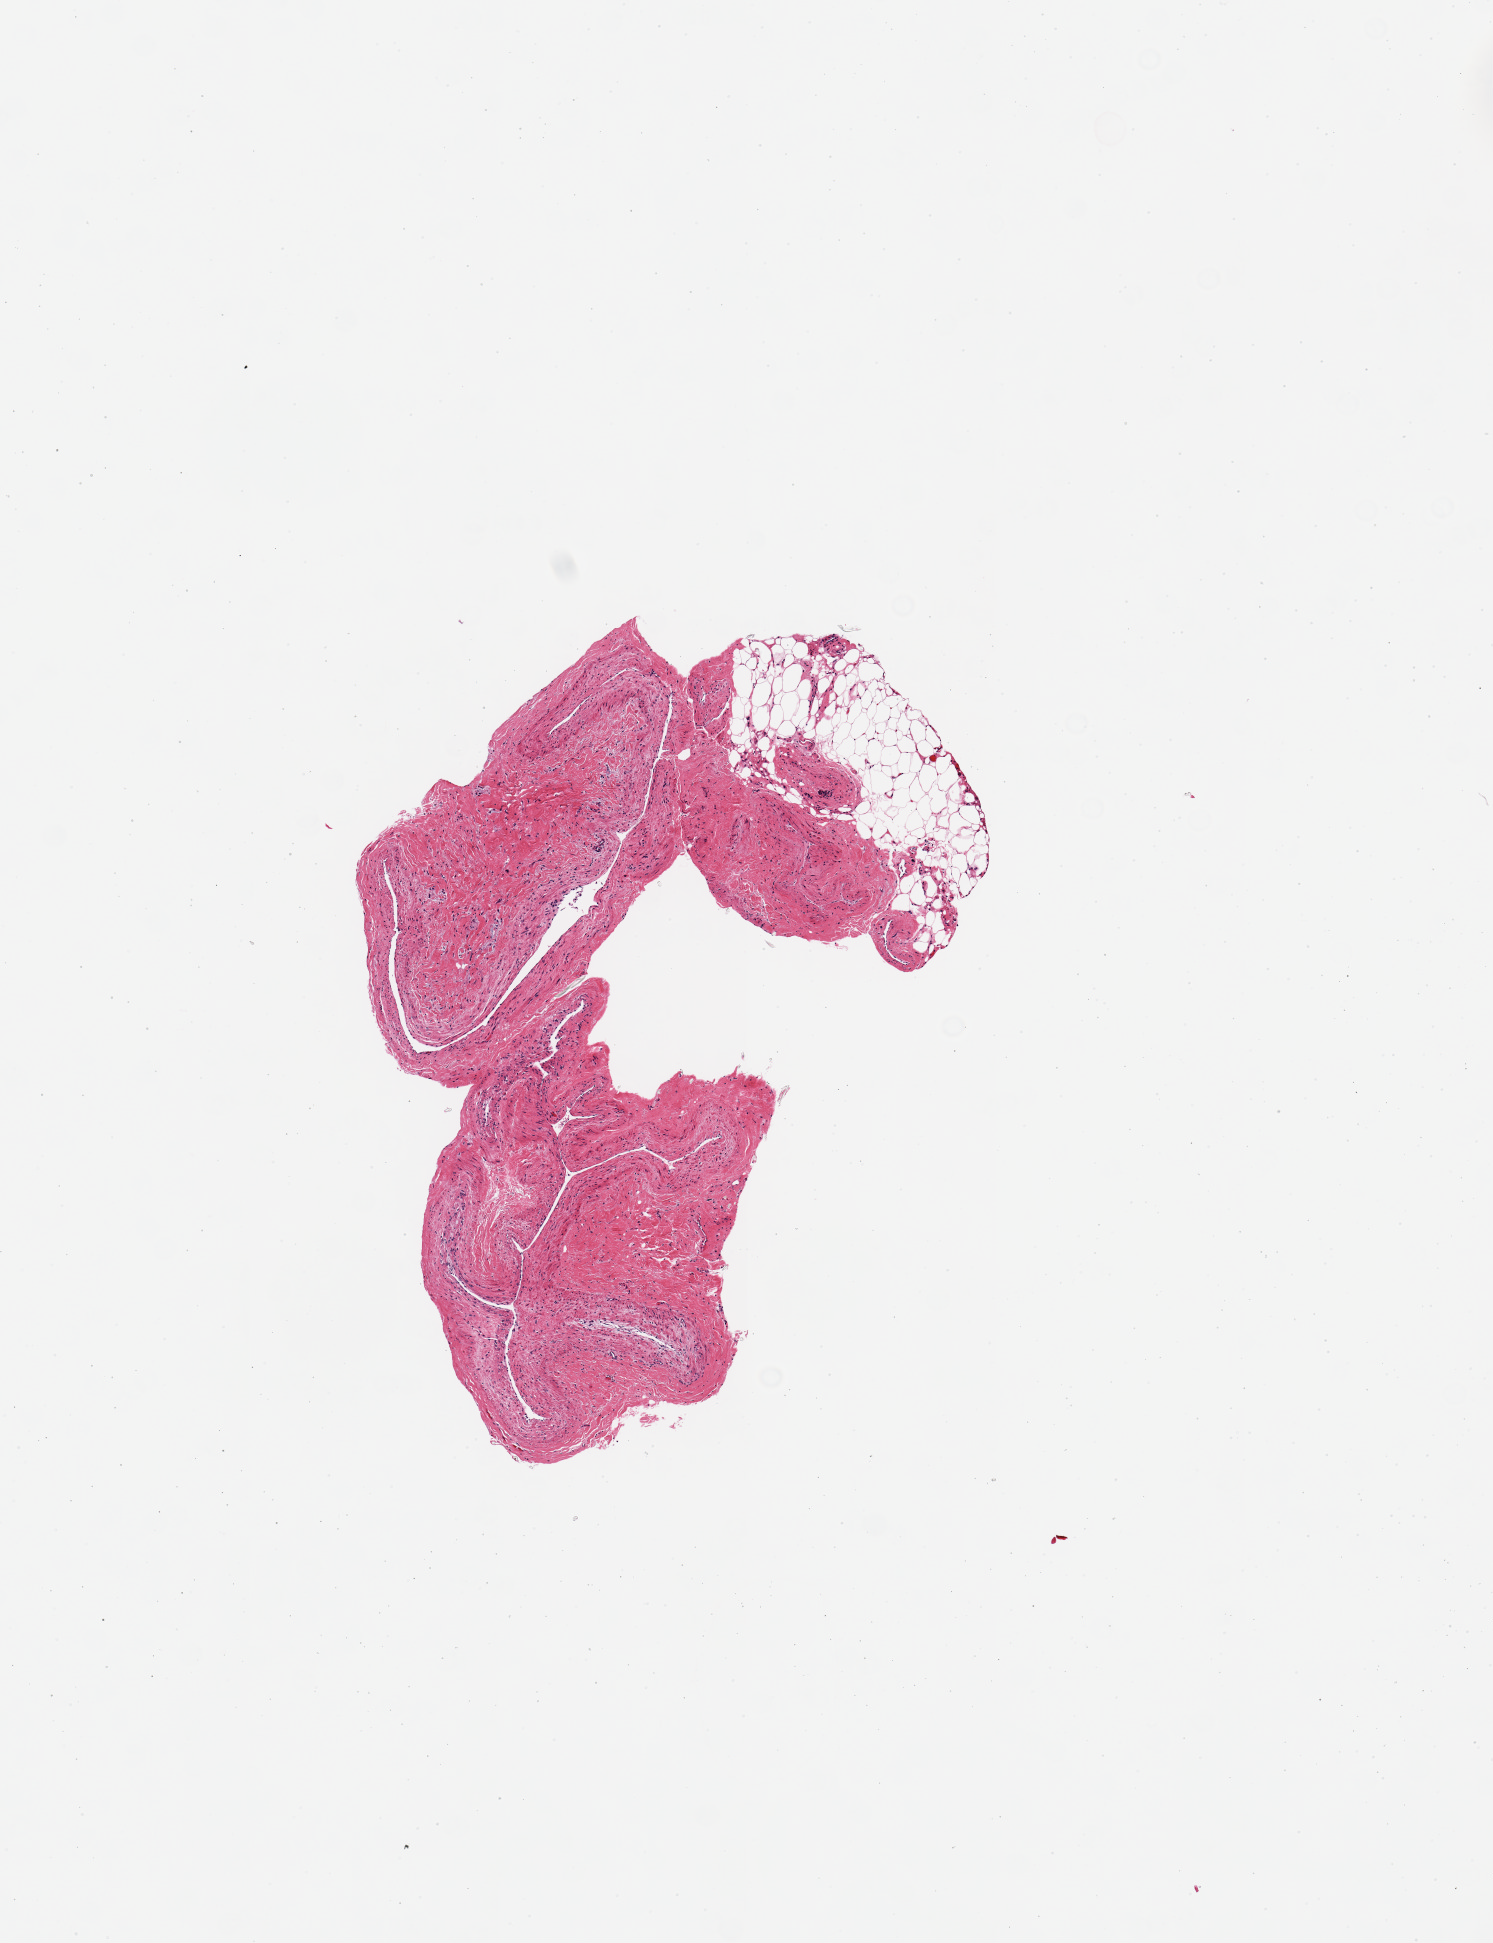
Whole-slide image, haematoxylin and eosin stain, shown as a low-resolution overview of the whole scanned area (about 5.9 x 7.7 mm); PAXgene-fixed, paraffin-embedded tissue; sampled site (target tissue): coronary artery; donor tissue sample. Donor sex: male.
Reviewer comment on this tissue sample: 1 piece, no coronary artery; probably sinus with myocardium/pericardial fat.